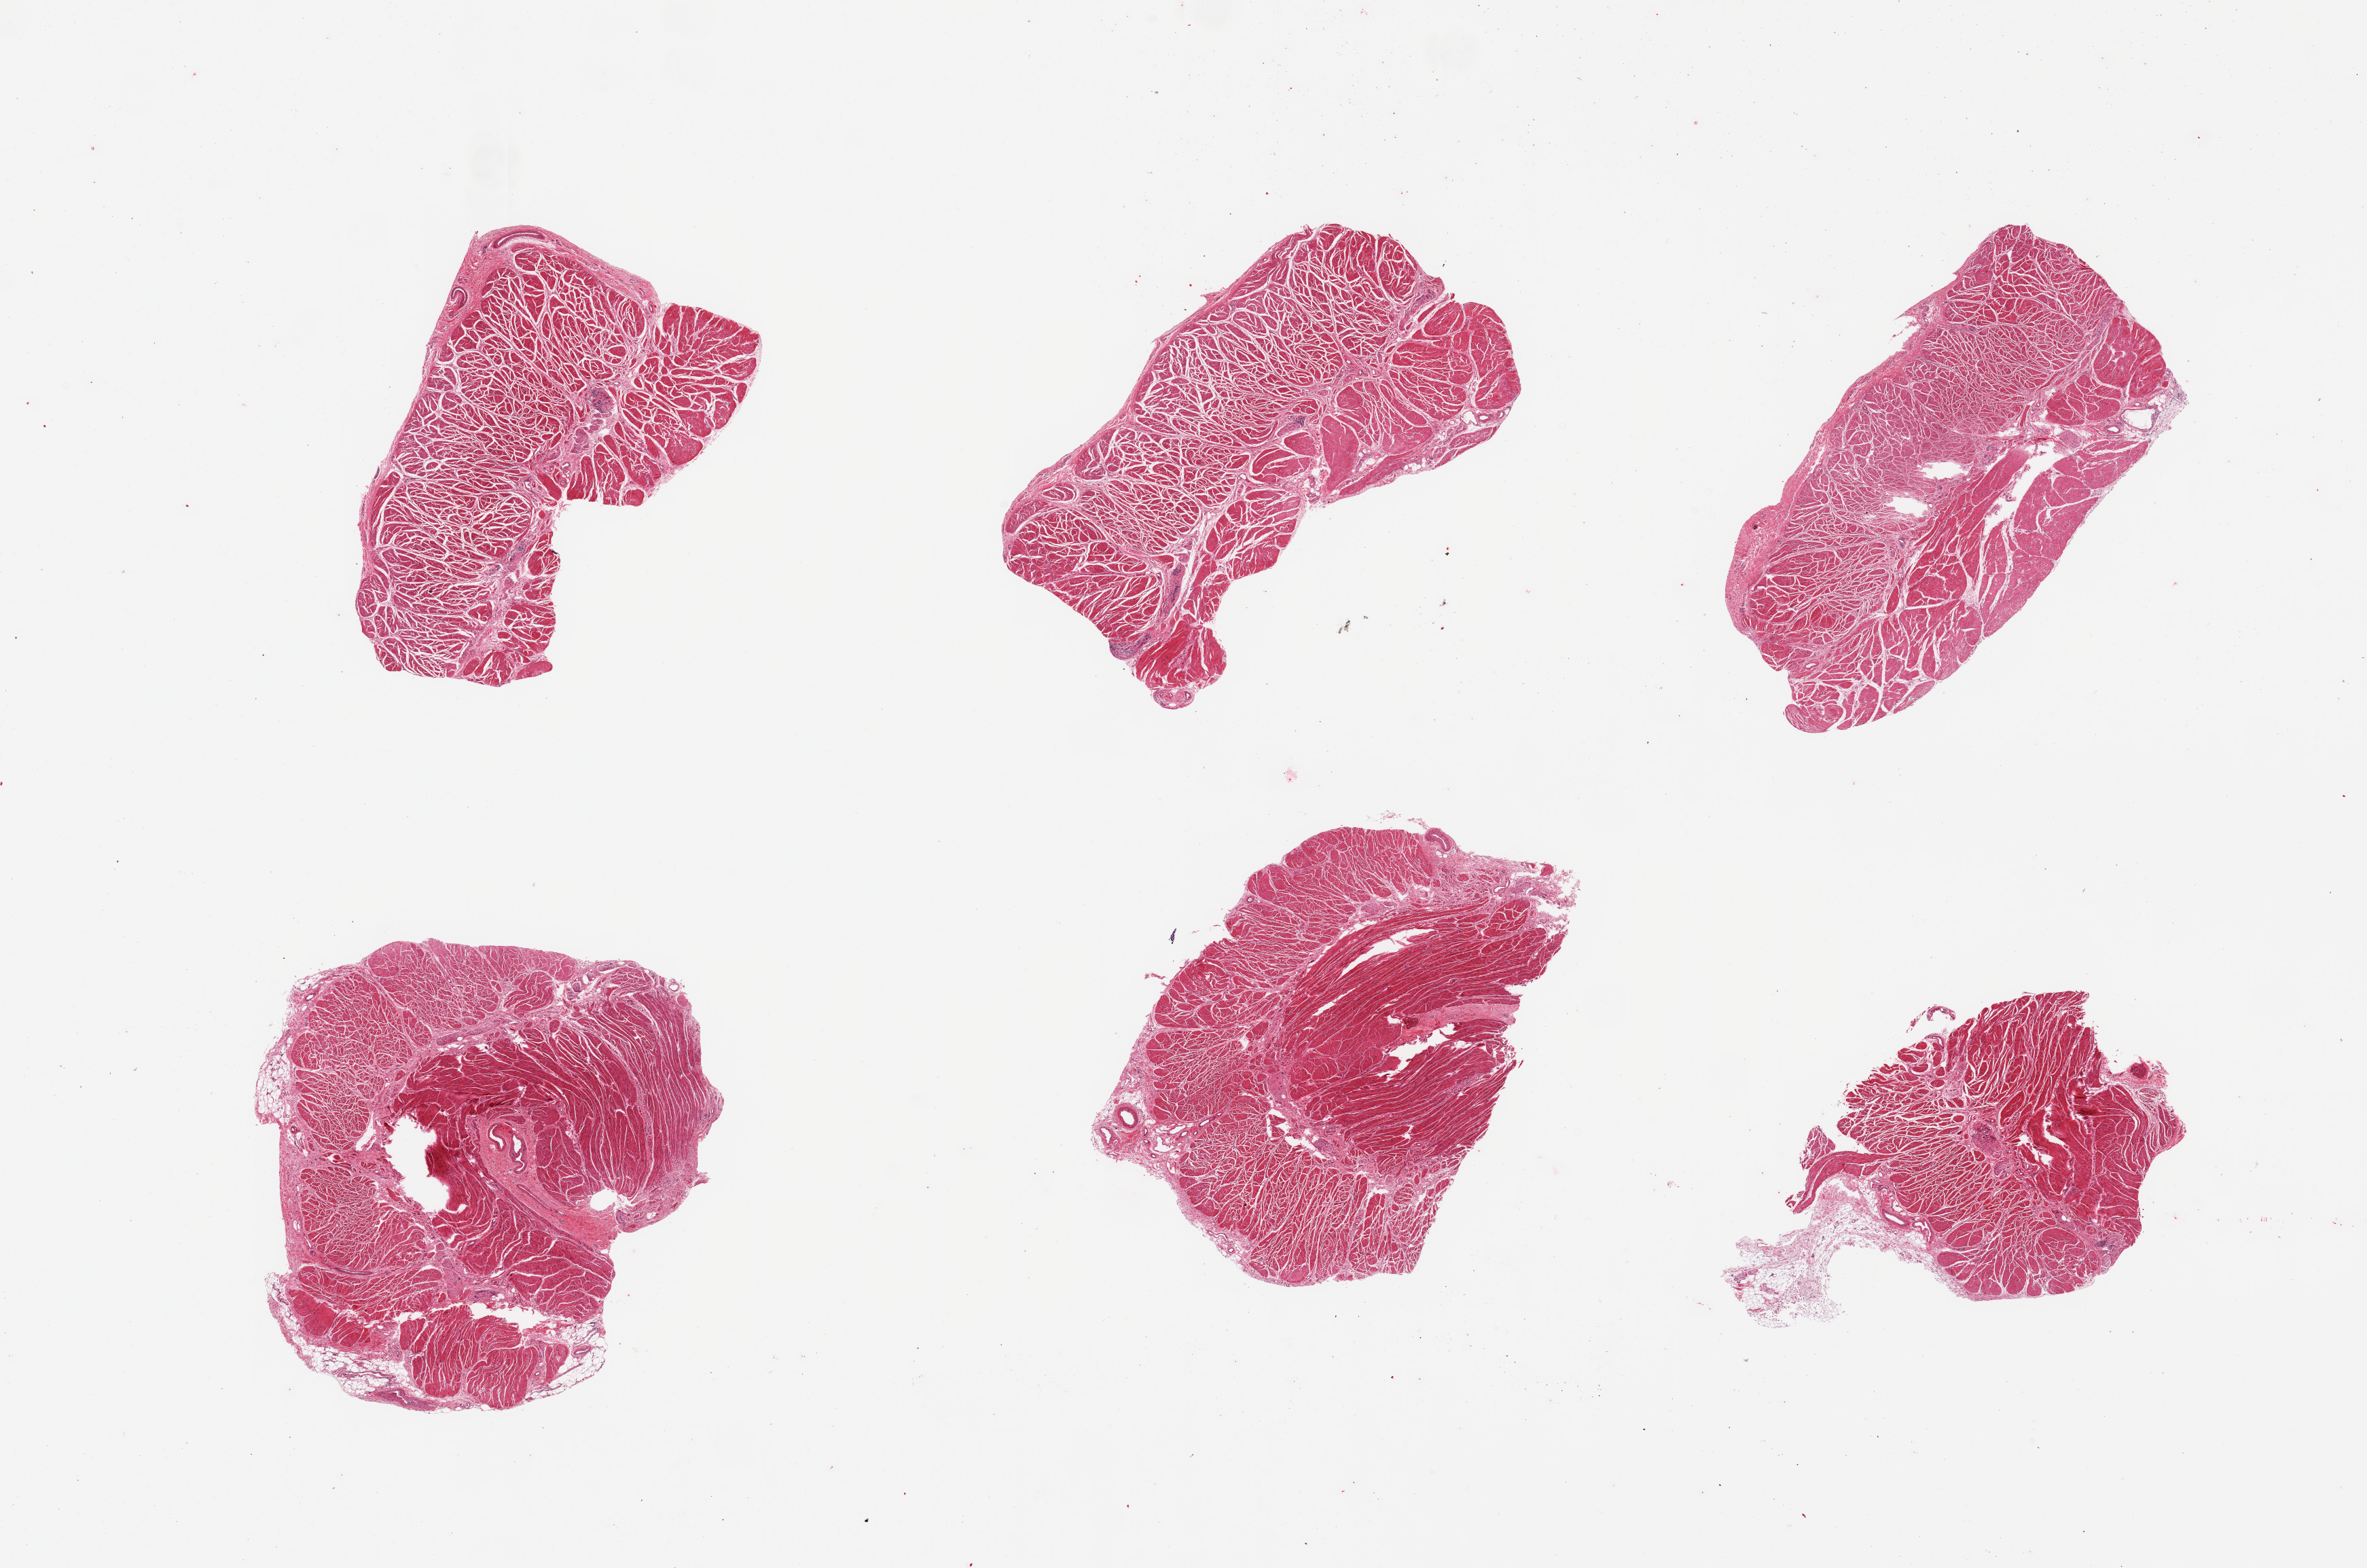
Digitized hematoxylin and eosin (H&E)-stained section, shown as a low-resolution overview of the whole scanned area (about 27.6 x 18.3 mm), PAXgene-fixed, paraffin-embedded tissue, target tissue: gastroesophageal junction, tissue donor sample. Donor: female.
Reviewer comment on this tissue sample: 6 pieces, confirmed target muscularis.